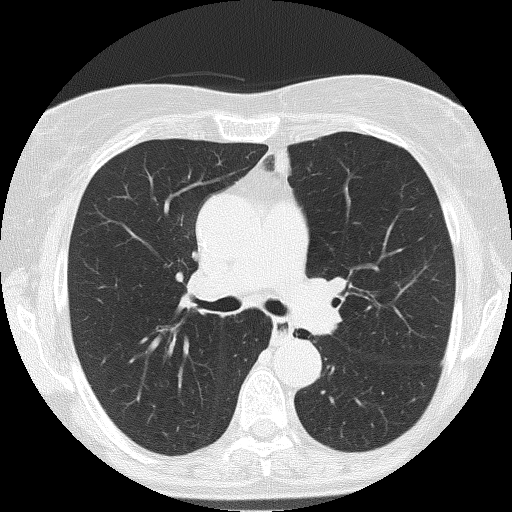
Low-dose screening chest CT, one axial slice; slice 108 of 166 in the series (ordered by position); reconstruction kernel FC51; 120 kVp; lung window (W 1500 / L -600 HU); 2 mm slice thickness; 512 × 512 image matrix.
Structures marked on this image (expert manual segmentation):
- lesion 2 (nodule, upper lobe of left lung): bounding box <274,151,289,176> (left, top, right, bottom; pixels)